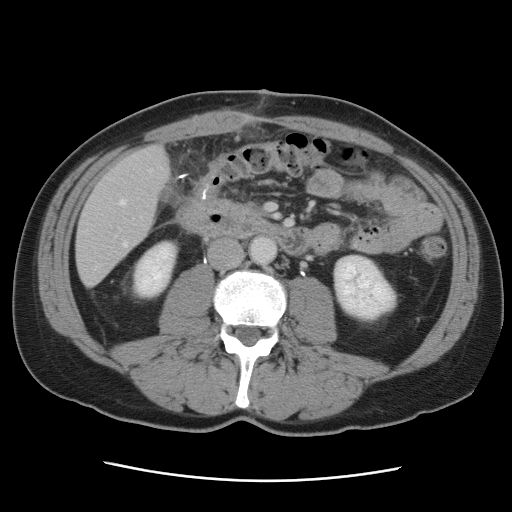
Contrast-enhanced abdominal CT, one axial slice. 120 kVp. Soft-tissue window (W 400 / L 40 HU). 512 × 512 image matrix, field of view 366 × 366 mm. Male patient, age 59 years. Case-level facts recorded for this patient, not image findings: diagnosis: colorectal cancer liver metastases, imaged before liver resection; multiple liver metastases: yes; largest metastasis: 0.6 cm; chemotherapy before resection: no.
Annotated regions visible in this slice (outlined manually by an expert reader):
- hepatic veins: bounding box (x1, y1, x2, y2) in pixels: (96, 170, 152, 269)
- liver: (77, 146, 169, 285)
- planned liver remnant (the part of the liver to remain after resection): (78, 146, 169, 253)